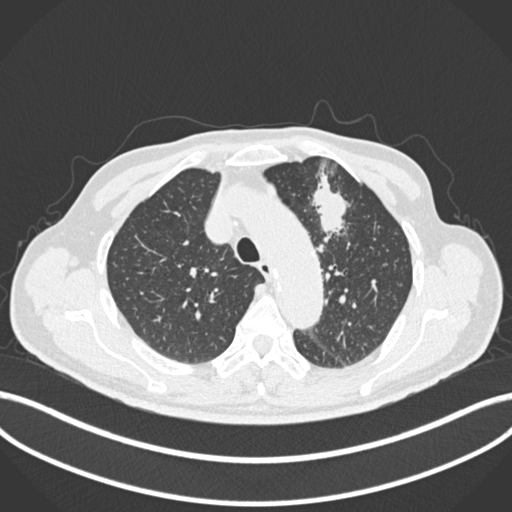
Chest CT, one axial slice. Slice 190 of 261 in the series (ordered by position). Reconstruction kernel B30f. Lung window (W 1500 / L -600 HU). 1 mm slice thickness. 512 × 512 image matrix, field of view 400 × 400 mm. Male patient, age 74 years. From the clinical record (not read from this slice): clinical TNM (as recorded): T2b N0 M1c.
Structures marked on this image (rectangle marked by the reading radiologist):
- lung tumour (recorded histology: adenocarcinoma): bounding box (x1, y1, x2, y2) in pixels: (308, 167, 356, 241)